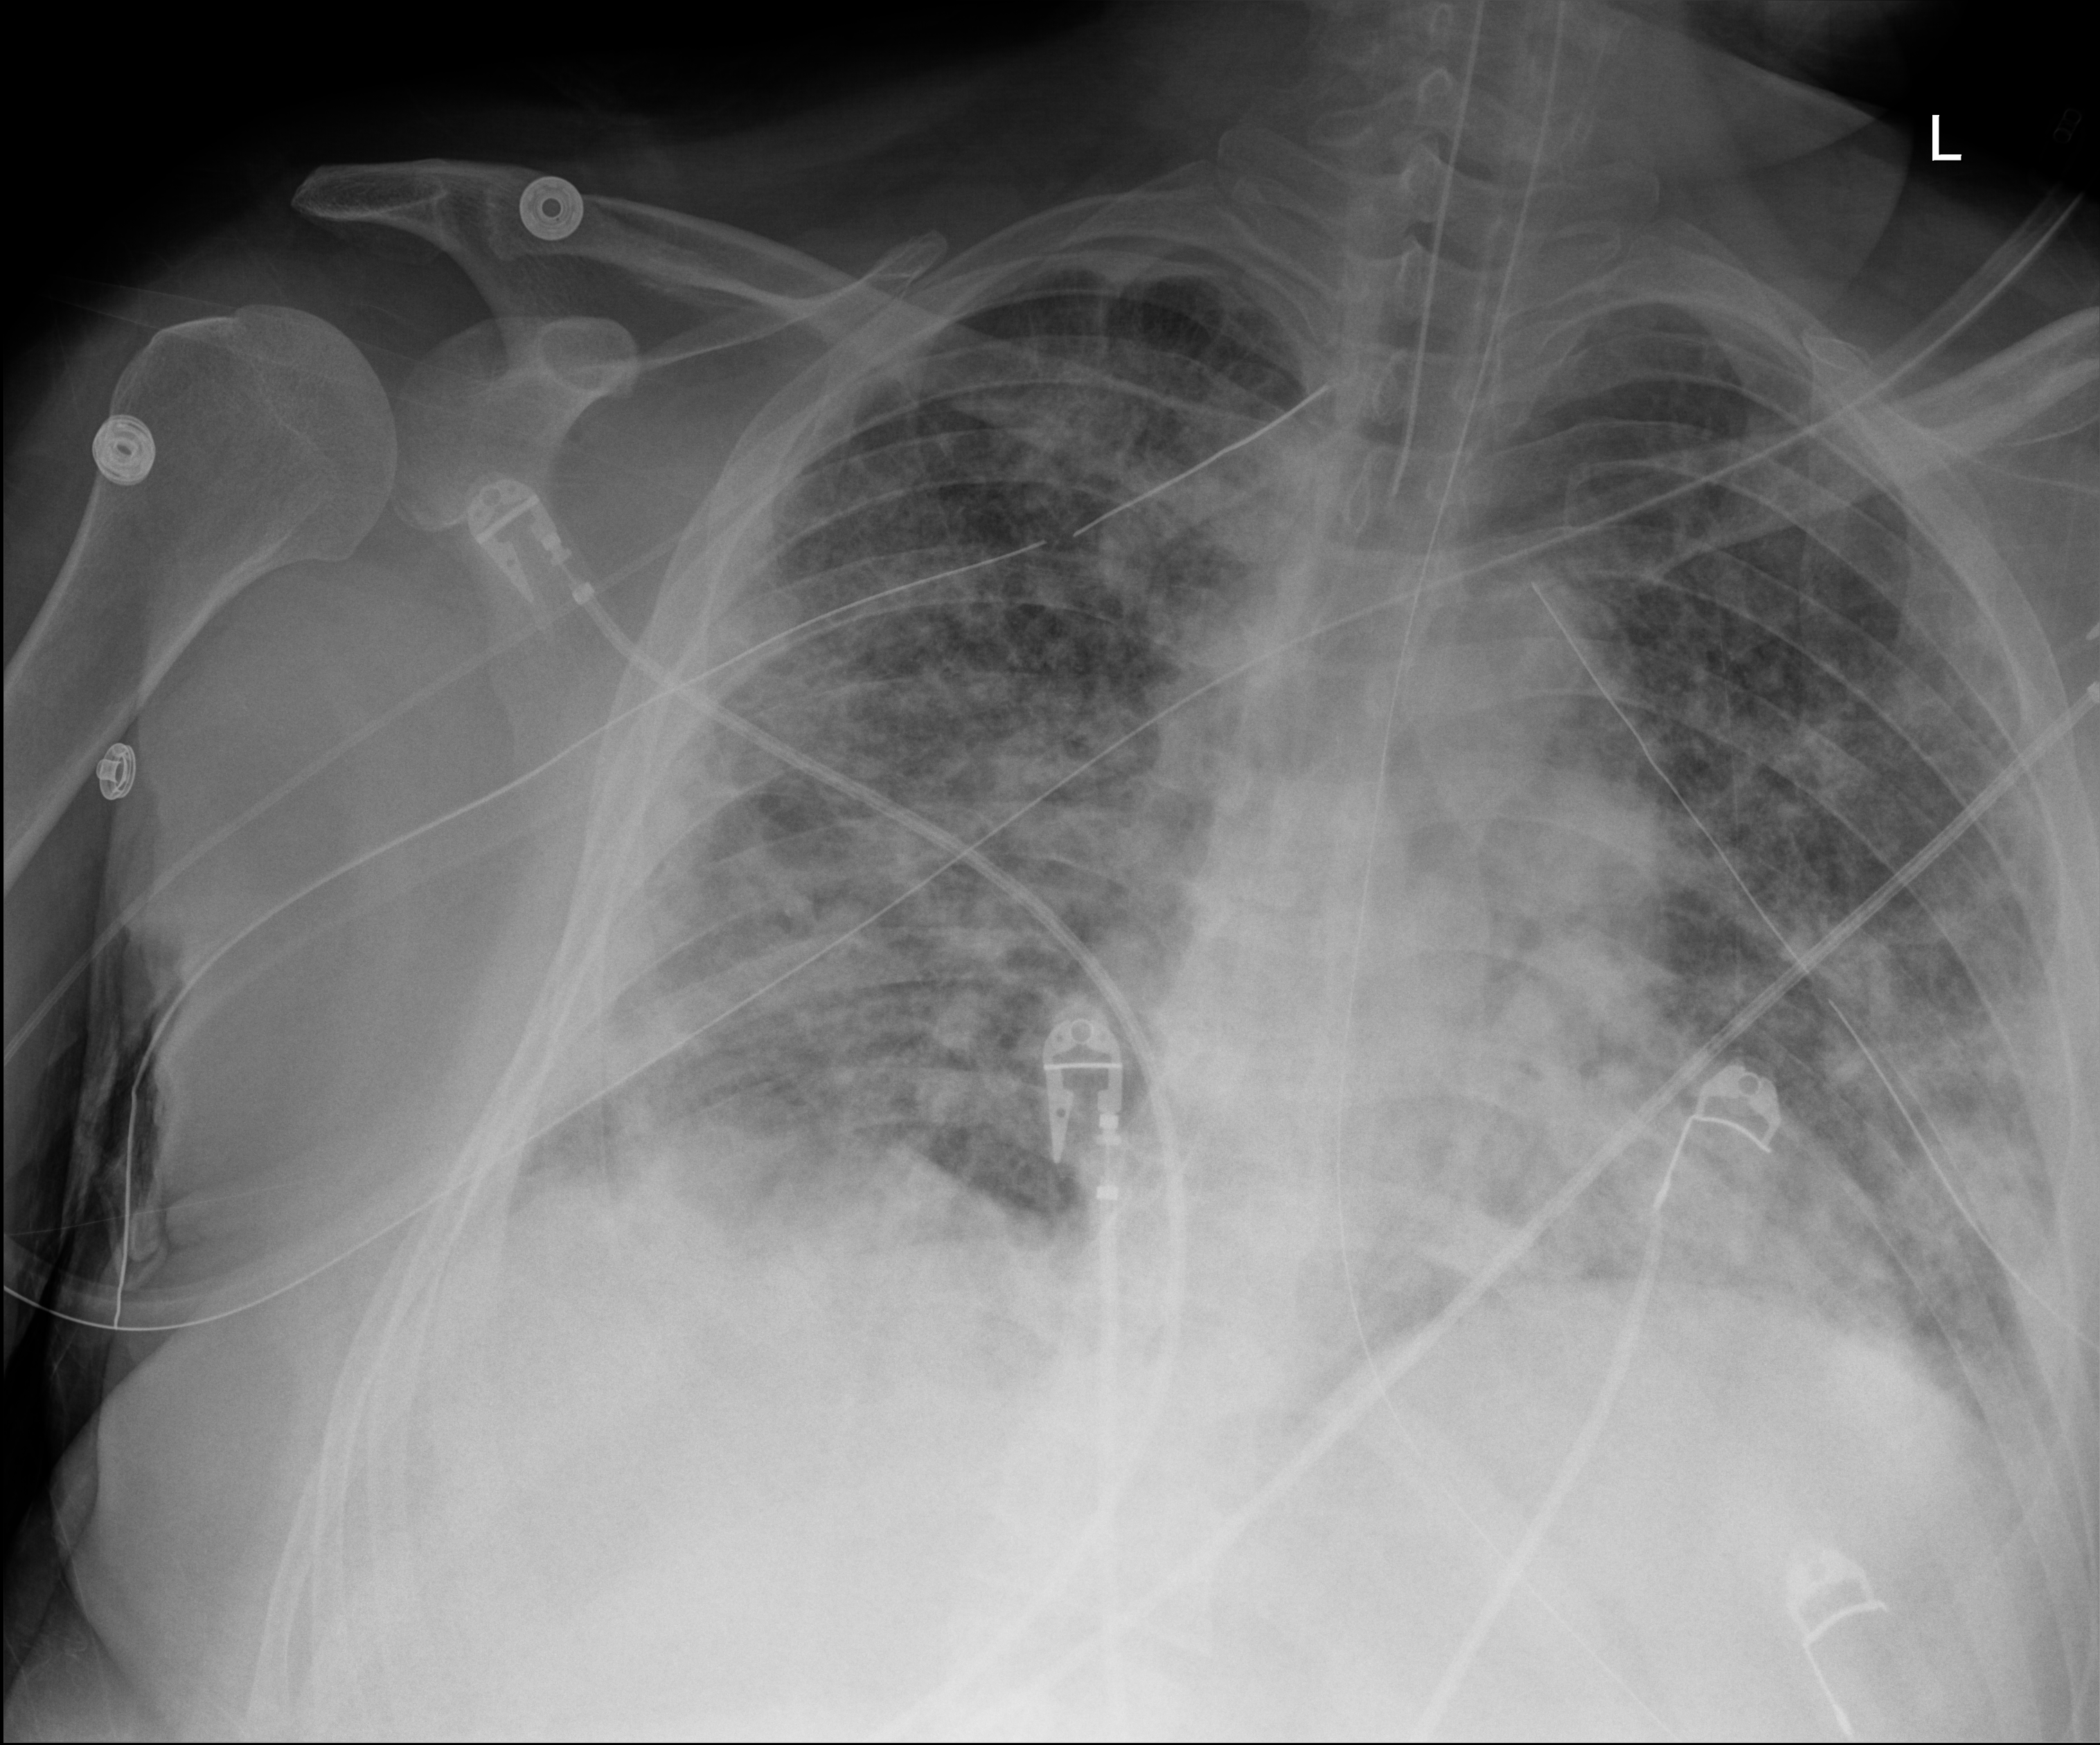
Portable chest radiograph, anteroposterior (AP) projection. Patient hospitalised with COVID-19; male, aged 18–59 years.
Hospital-stay facts (about this admission, not read from this image; timing relative to this image not recorded): other chronic lung disease (admission record): no.